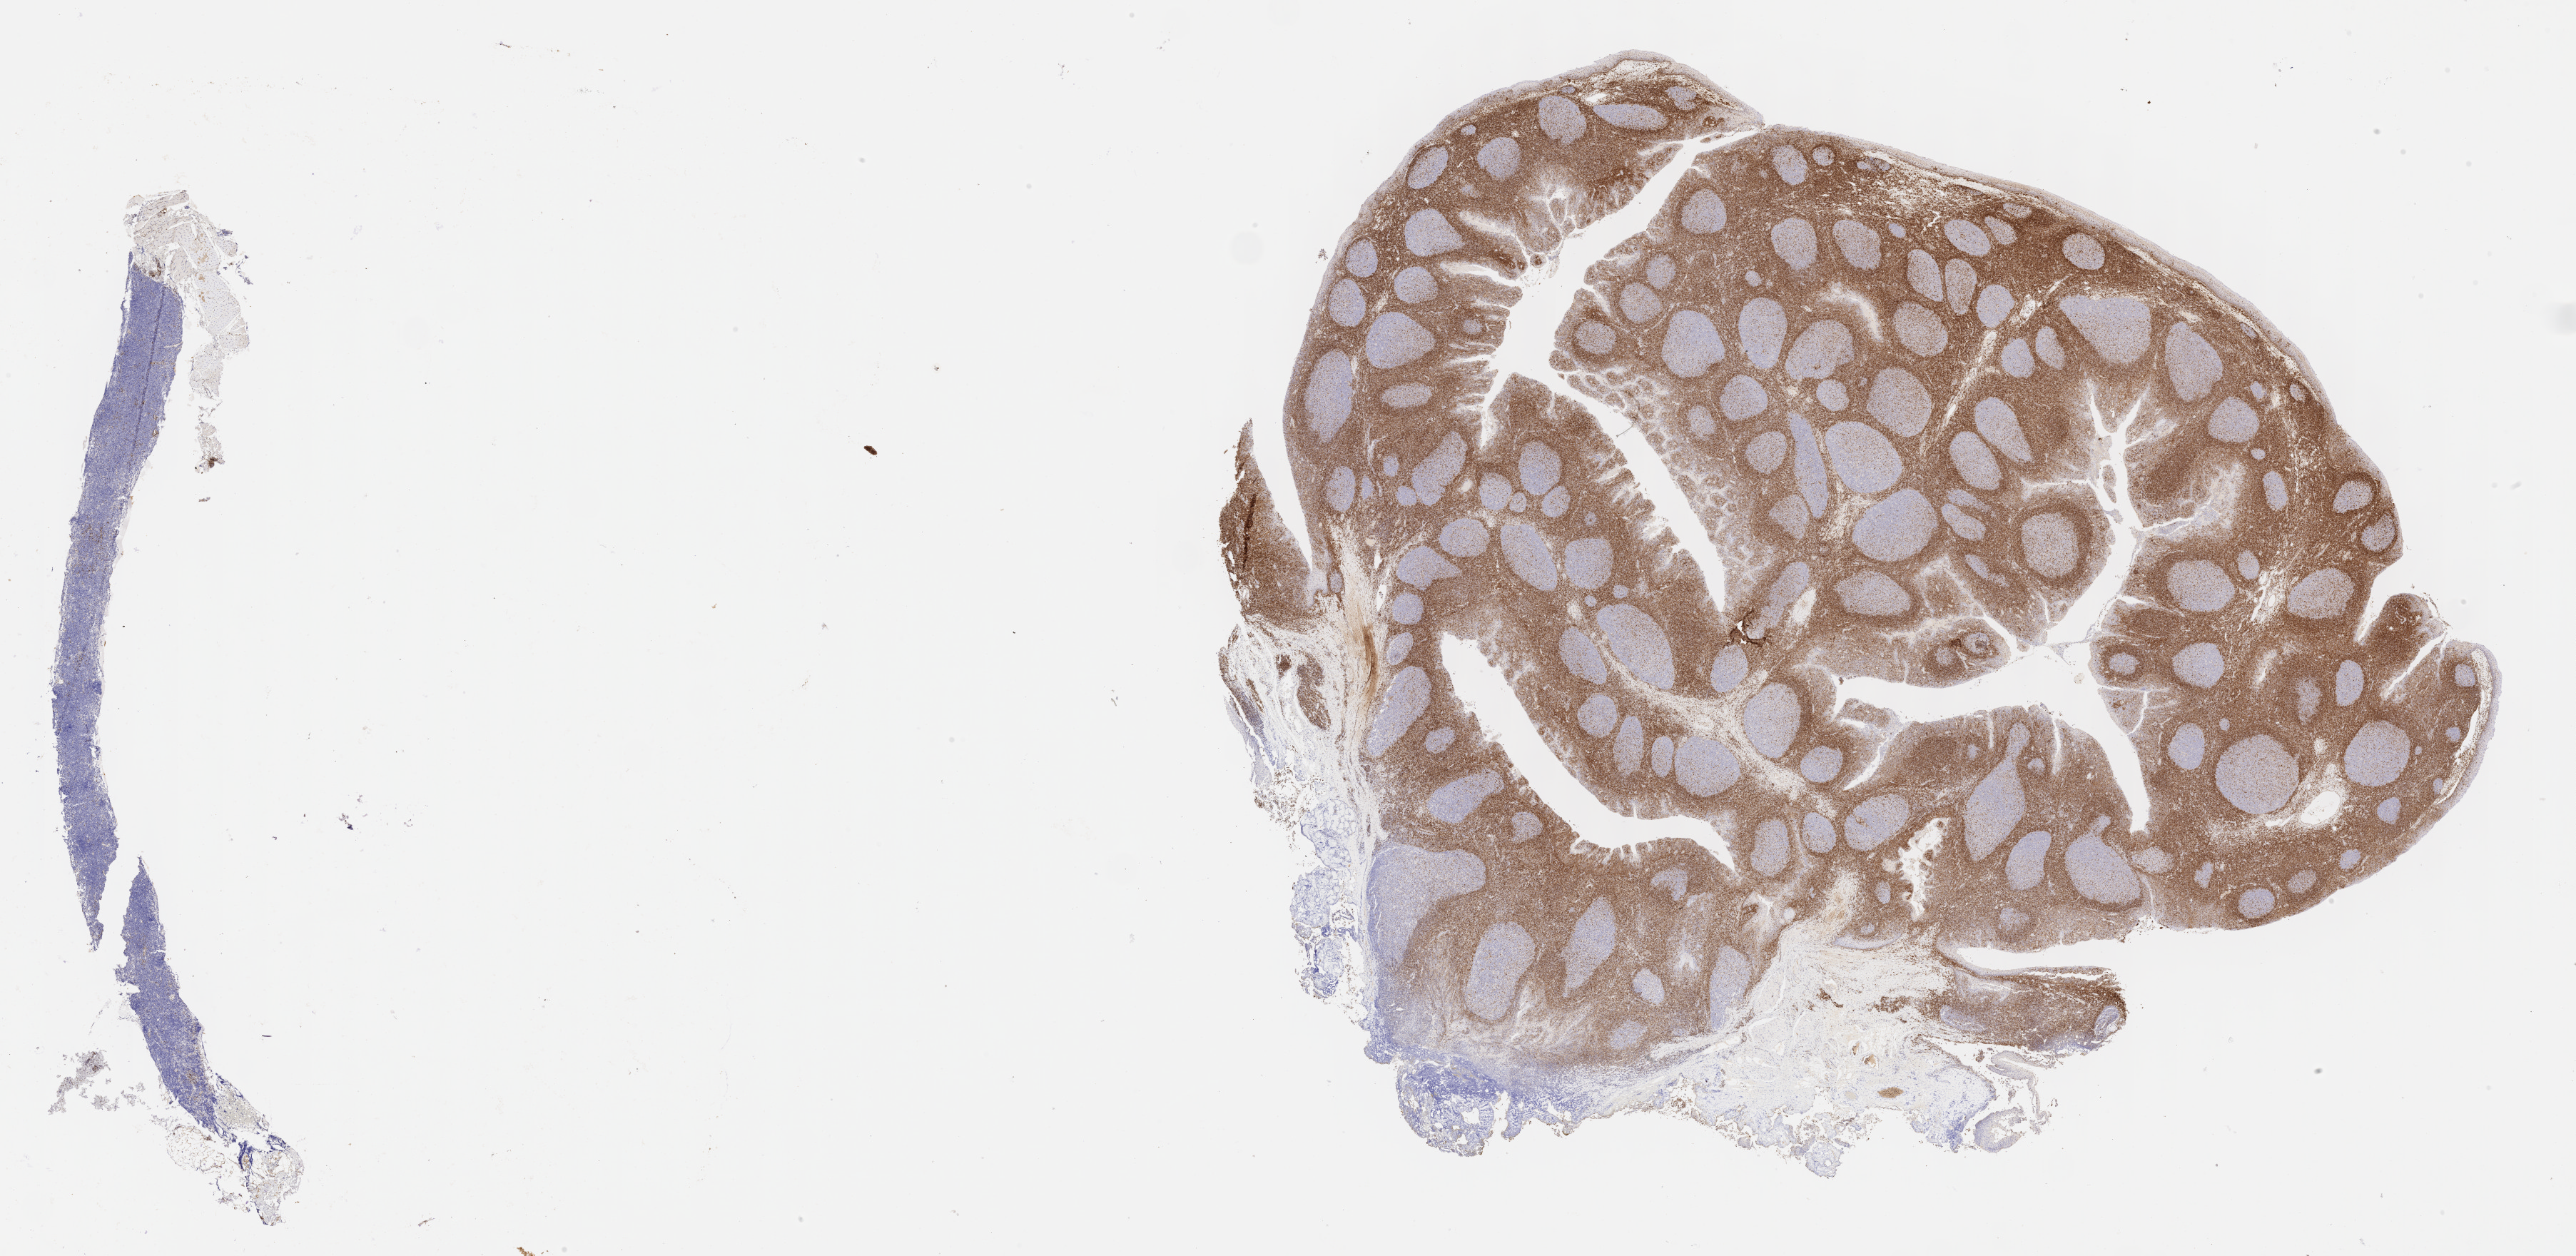
IHC for BCL2, whole-slide image — a low-resolution overview of the entire scanned area, about 29.2 x 14.2 mm. Tumor tissue. Site: cranium. Female patient; age at initial diagnosis 7 years.
* histologic diagnosis: Burkitt lymphoma, NOS